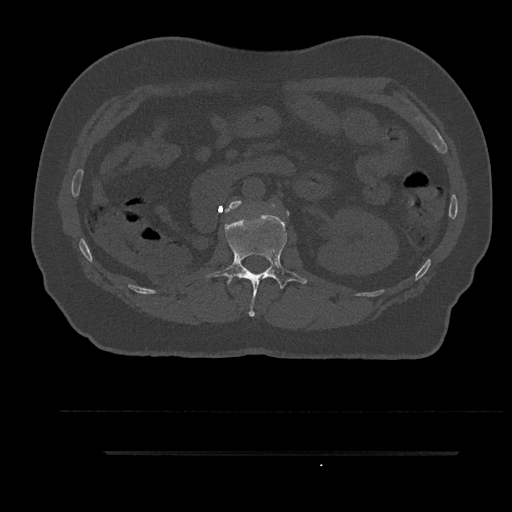
CT including the spine, one axial slice; slice 169 of 797 in the series (ordered by position); reconstruction kernel Br40s/3; bone window (W 1800 / L 400 HU); 0.5 mm slice thickness; 512 × 512 image matrix, field of view 432 × 432 mm. Patient: male, 63 years. Case-level facts recorded for this patient, not image findings: primary cancer: renal.
Structures marked on this image (semi-automatic segmentation, software-assisted and operator-edited):
- L1 vertebra: bounding box (x1, y1, x2, y2) in pixels: (205, 214, 307, 317)
- L2 vertebra: (225, 201, 289, 215)